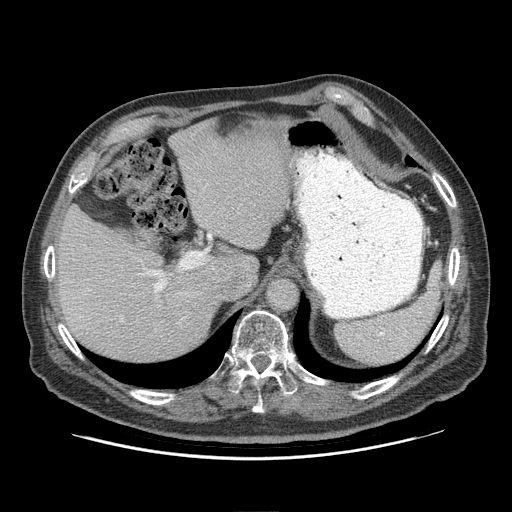
Contrast-enhanced abdominal CT (liver protocol), one axial slice. Position 65 of 95 along the scan axis. 140 kVp. Soft-tissue window (W 400 / L 40 HU). 512 × 512 image matrix, field of view 400 × 400 mm. Case-level facts recorded for this patient, not image findings: diagnosis: hepatocellular carcinoma (patient treated with transarterial chemoembolisation; whether this scan precedes or follows treatment is not stated here); TNM stage (as recorded): Stage-IVB; Child-Pugh class: A; tumour differentiation: well differentiated; tumour nodularity: uninodular.
Structures marked on this image (semi-automatic segmentation, software-assisted and operator-edited):
- abdominal aorta: box from (x=267, y=279) to (x=297, y=310) px
- liver parenchyma outside the tumour (the mass and vessels are separate outlines, so this box may not span the whole liver): (x=56, y=119)–(x=294, y=360)
- liver vessels: (x=148, y=264)–(x=192, y=292)